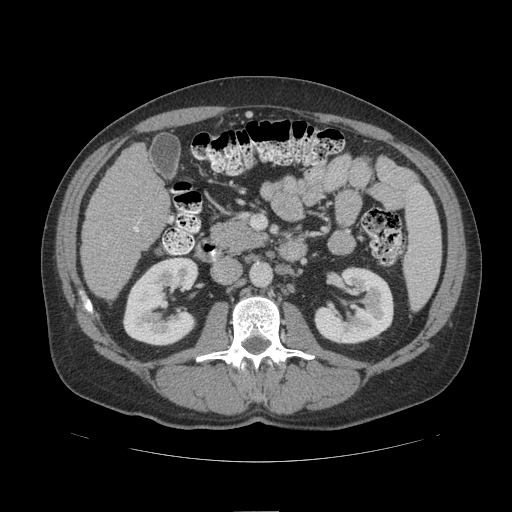
Contrast-enhanced abdominal CT (liver protocol), one axial slice. Position 42 of 109 along the scan axis. Reconstruction kernel STANDARD. 140 kVp. Soft-tissue window (W 400 / L 40 HU). 512 × 512 image matrix, field of view 420 × 420 mm. Case-level facts recorded for this patient, not image findings: diagnosis: hepatocellular carcinoma (patient treated with transarterial chemoembolisation; whether this scan precedes or follows treatment is not stated here); TNM stage (as recorded): Stage-IIIB; Child-Pugh class: A; tumour differentiation: poorly differentiated; tumour nodularity: multinodular.
Annotated regions visible in this slice (semi-automatic segmentation, software-assisted and operator-edited):
- liver parenchyma outside the tumour (the mass and vessels are separate outlines, so this box may not span the whole liver): bounding box <80,144,170,300> (left, top, right, bottom; pixels)
- liver vessels: <134,227,139,232>